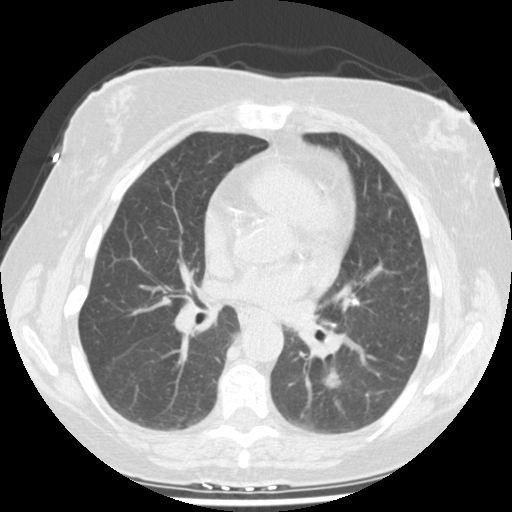
Low-dose screening chest CT, one axial slice; position 91 of 159 along the scan axis; lung window (W 1500 / L -600 HU); 2.5 mm slice thickness; 512 × 512 image matrix, field of view 326 × 326 mm.
Outlined on this slice (manually delineated by an expert):
- lesion 1 (tumor, lower lobe of left lung): bounding box <323,368,342,389> (left, top, right, bottom; pixels)